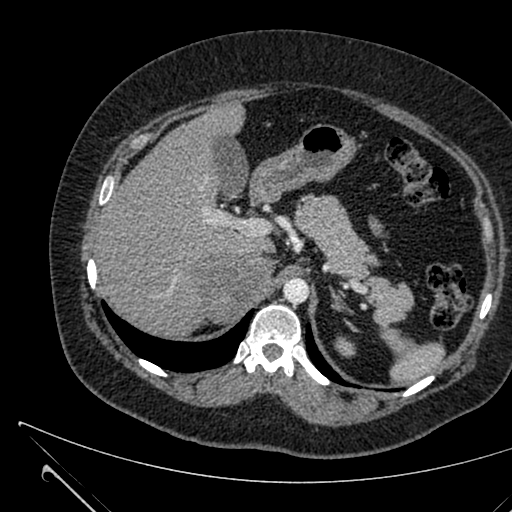
Contrast-enhanced abdominal CT, one axial slice. Slice 461 of 731 in the series (ordered by position). 120 kVp. Intravenous contrast given. Soft-tissue window (W 400 / L 40 HU). 512 × 512 image matrix, field of view 376 × 376 mm. Patient: female, 36 years. From the clinical record (not read from this slice): diagnosis: adrenocortical carcinoma; tumour side: right adrenal; tumour size at pathology: 10 cm; Ki-67 index: 20 %; stage (as recorded): 4.
Outlined on this slice (semi-automatically segmented with operator editing):
- mass: box from (x=202, y=257) to (x=269, y=322) px